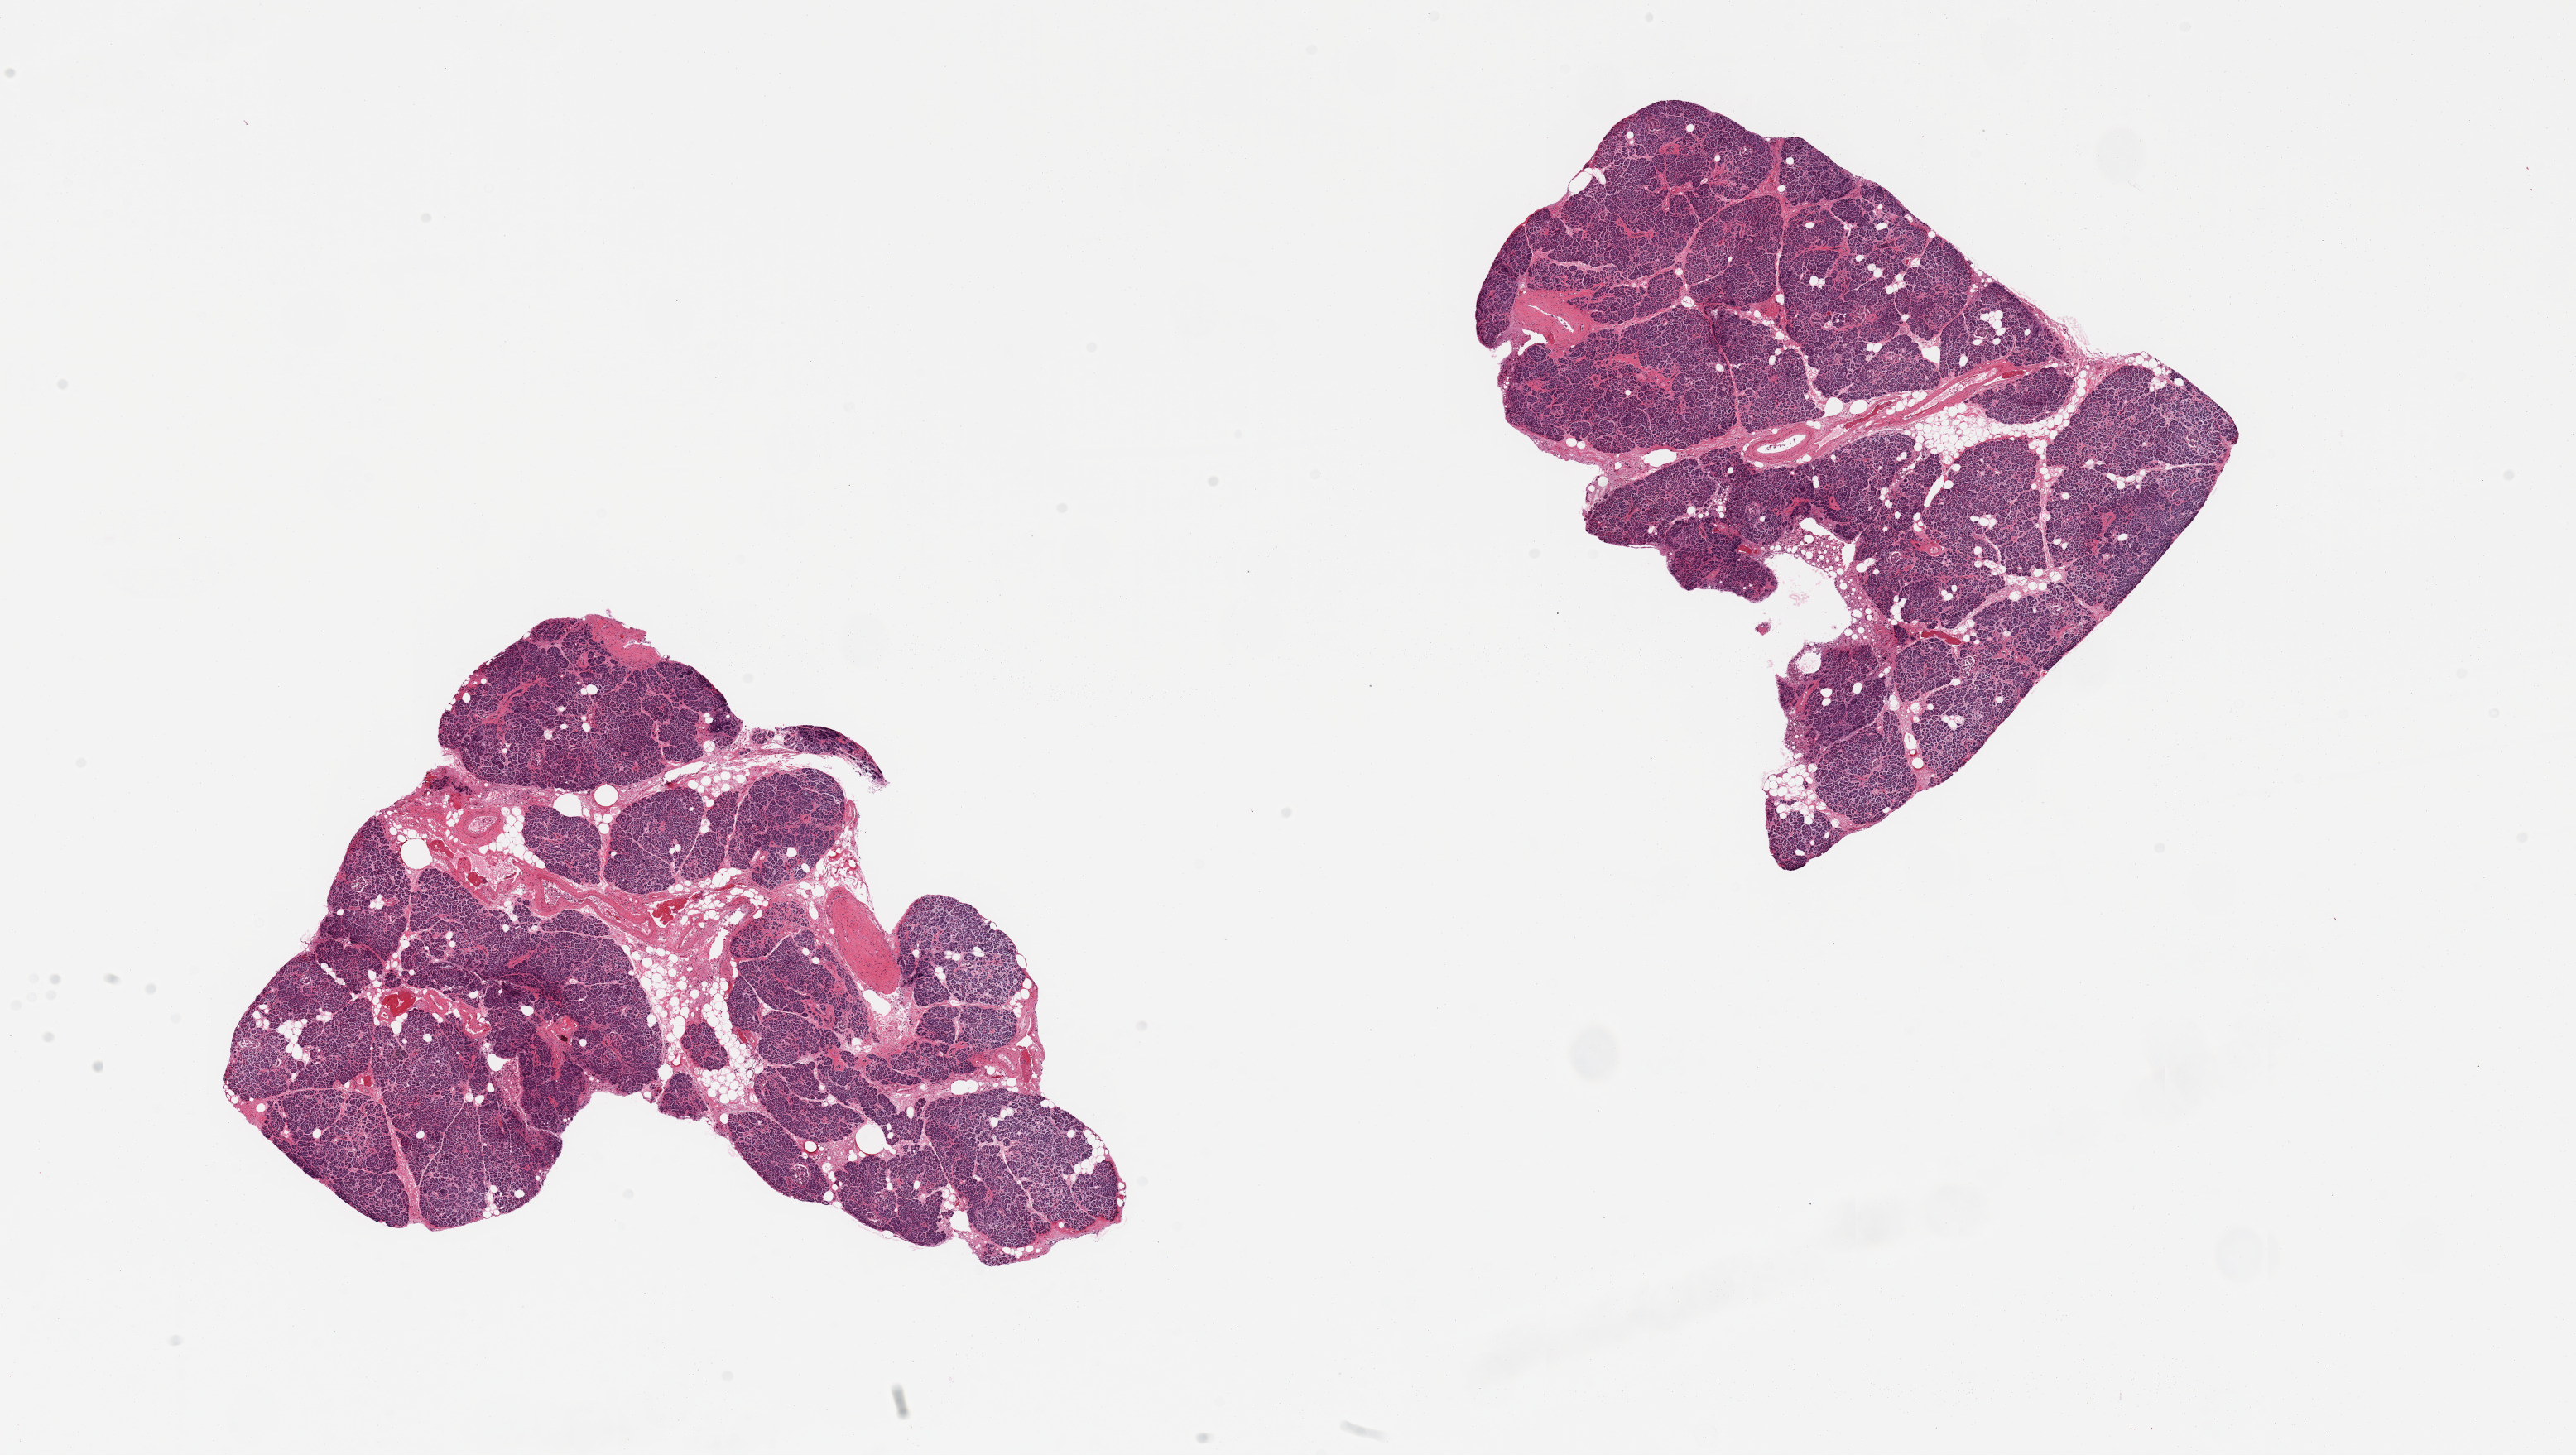
Digitized haematoxylin and eosin-stained section, a low-resolution overview of the entire scanned area, about 24.6 x 13.9 mm; PAXgene-fixed, paraffin-embedded tissue; section of pancreas (target tissue); donor tissue sample. Female donor.
- review note (as recorded): 2 pieces; 10 and 25 % internal fat